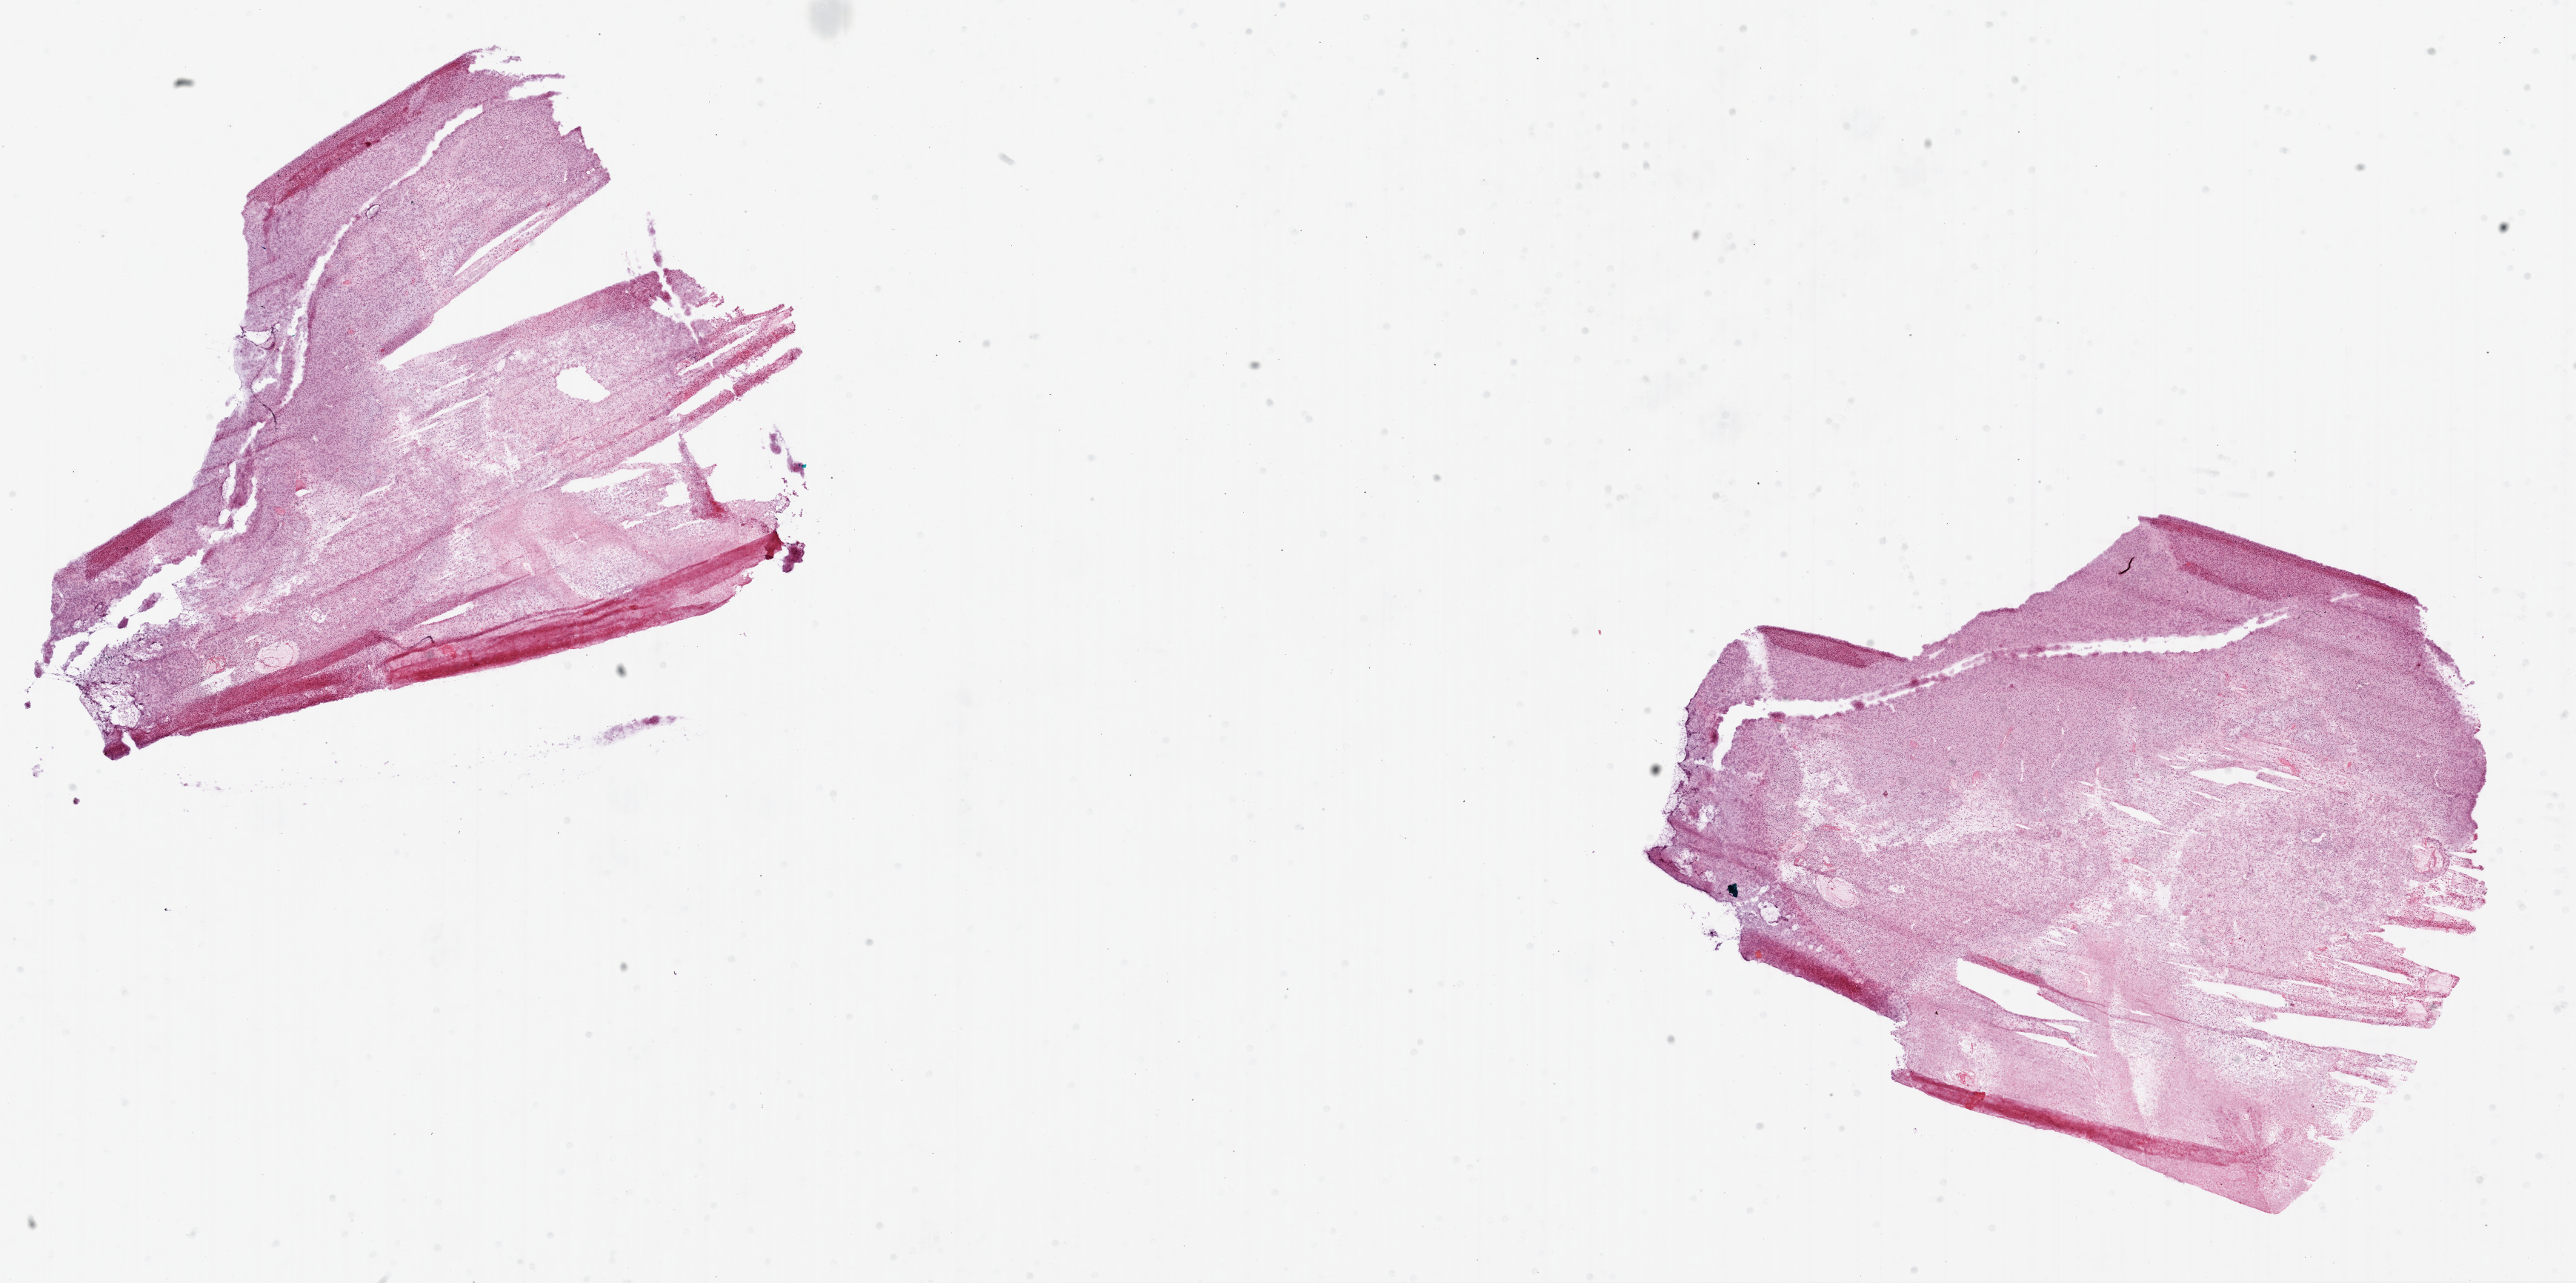
Digitized H&E-stained tissue section (whole slide) — a low-resolution overview of the entire scanned area, about 28.0 x 14.0 mm; frozen section from the bottom of the tissue portion; sample: primary tumour, brain. Patient: male, age at initial diagnosis 58 years. Slide review estimates, as recorded: tumour cells 65%, tumour nuclei 95%, normal cells 0%, stromal cells 0%, necrosis 30%. Infiltration values recorded for this section: lymphocyte infiltration 0%, monocyte infiltration 0%, neutrophil infiltration 0%.
Pathologic diagnosis: Glioblastoma.